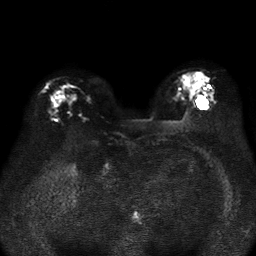
Breast MRI, one axial slice; position 18 of 37 along the scan axis; diffusion-weighted series; image 2 of 4 stored at this slice position (different b-values; order by instance number); 1.5 T; 5 mm slice thickness; 256 × 256 image matrix, field of view 320 × 320 mm. Female patient.
Structures marked on this image (outlined manually by an expert reader):
- tumour on diffusion-weighted imaging: box from (x=67, y=88) to (x=75, y=101) px